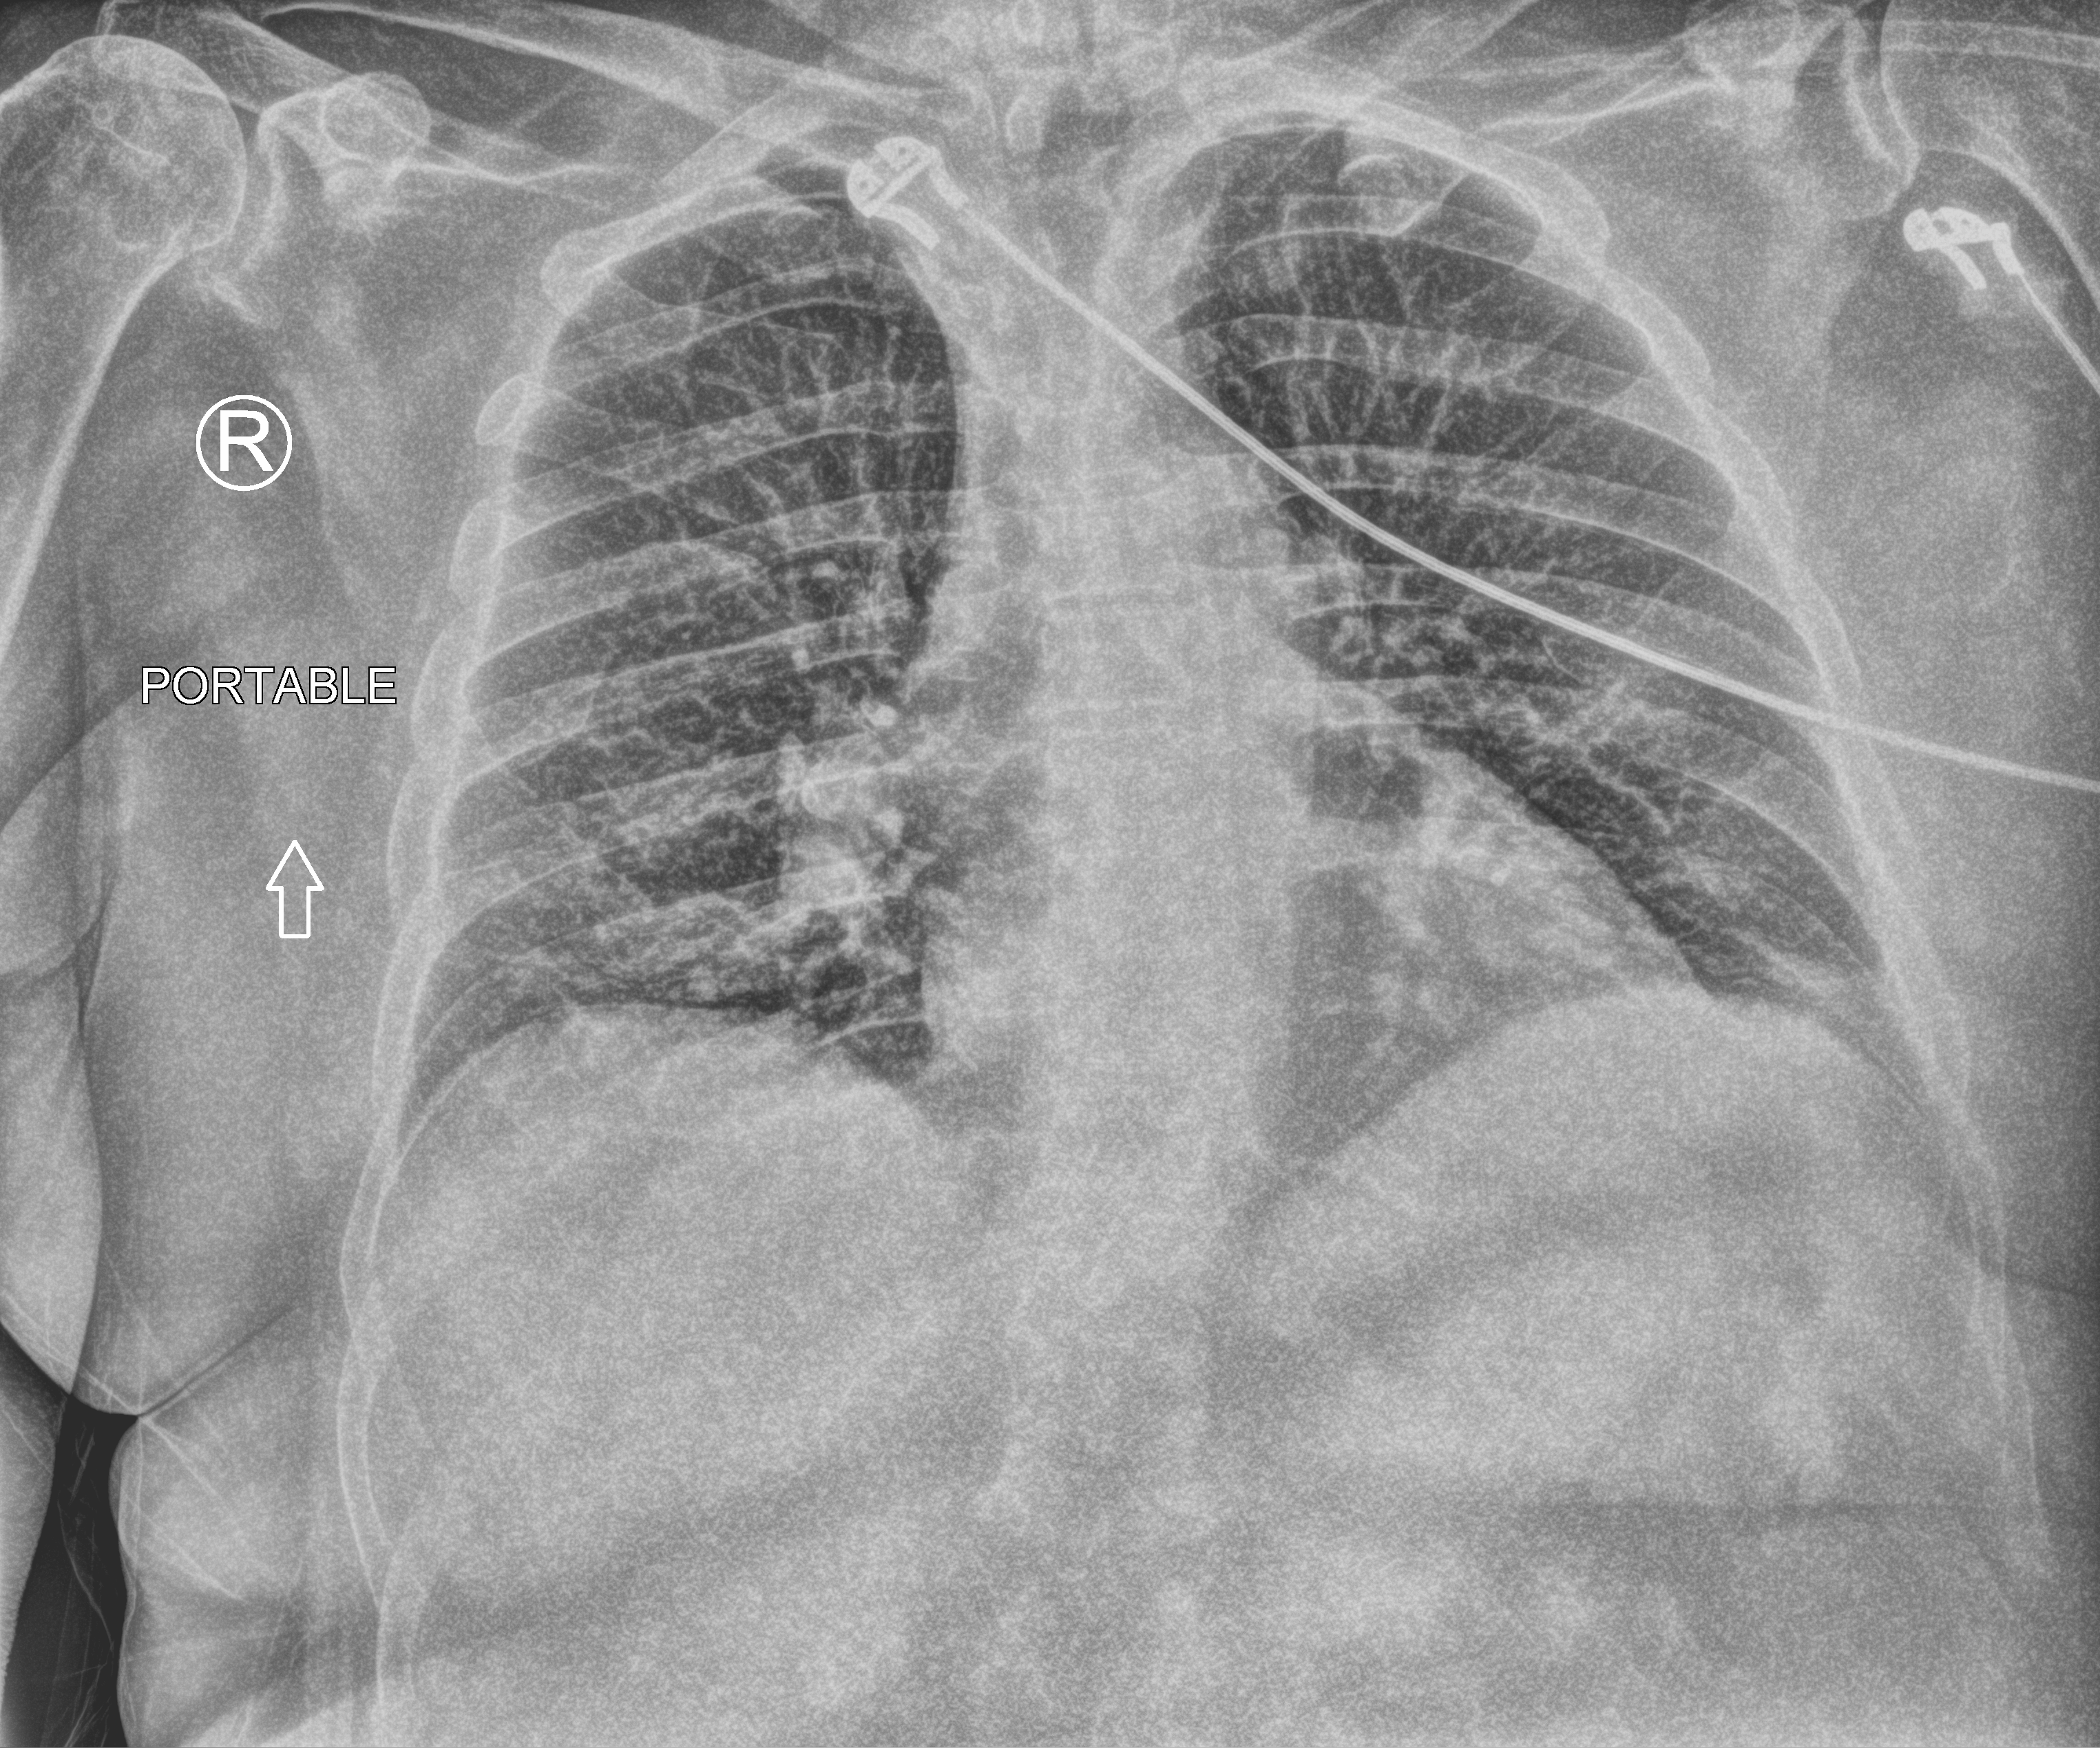
Chest X-ray (portable); anteroposterior (AP) projection. Patient hospitalised with COVID-19; male, aged 60–74 years.
Admission-level facts for this patient (not findings on this image; timing relative to this image not recorded):
- mechanically ventilated during this hospital stay: no
- admitted to intensive care during this hospital stay: no
- hypertension (admission record): no